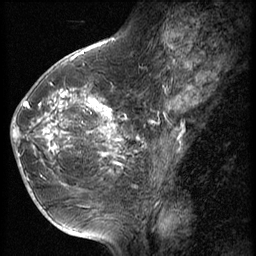
Breast MRI (dynamic contrast-enhanced), one sagittal slice. Position 26 of 56 along the scan axis. 3 images stored at this slice position (order not interpretable as contrast timing). 1.5 T. TE 4.2 ms, TR 9 ms. 2.5 mm slice thickness. 256 × 256 image matrix, field of view 180 × 180 mm. Patient: female, 49 years. Case-level facts recorded for this patient, not image findings: setting: breast cancer imaged before/during neoadjuvant chemotherapy; receptor status: HER2-positive.
Structures marked on this image (semi-automatic segmentation, software-assisted and operator-edited):
- analysis volume of interest (the breast-tissue region the enhancement analysis was run in; not a lesion): bounding box [x1, y1, x2, y2] px = [13, 79, 131, 203]
- tumour enhancement mask (voxels above the 140 % enhancement threshold inside the analysis volume of interest): [13, 89, 126, 173]